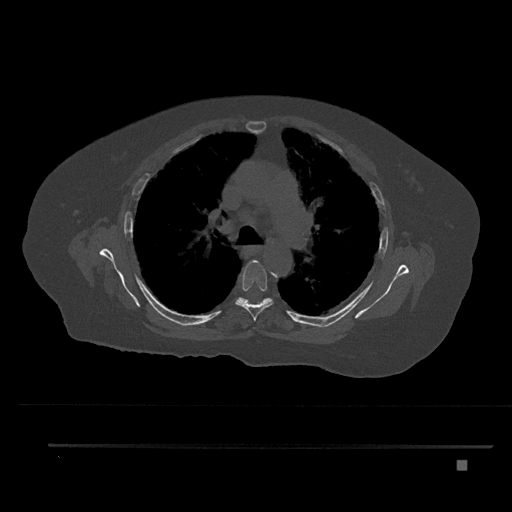
CT including the spine, one axial slice. Position 562 of 797 along the scan axis. Bone window (W 1800 / L 400 HU). 512 × 512 image matrix, field of view 437 × 437 mm. Patient: female, 76 years. From the clinical record (not read from this slice): primary cancer: lung; vertebrae with lytic lesions (as recorded): T11, L3.
Structures marked on this image (semi-automatic segmentation, software-assisted and operator-edited):
- T5 vertebra: bounding box <235,261,274,321> (left, top, right, bottom; pixels)
- T6 vertebra: <236,297,272,305>